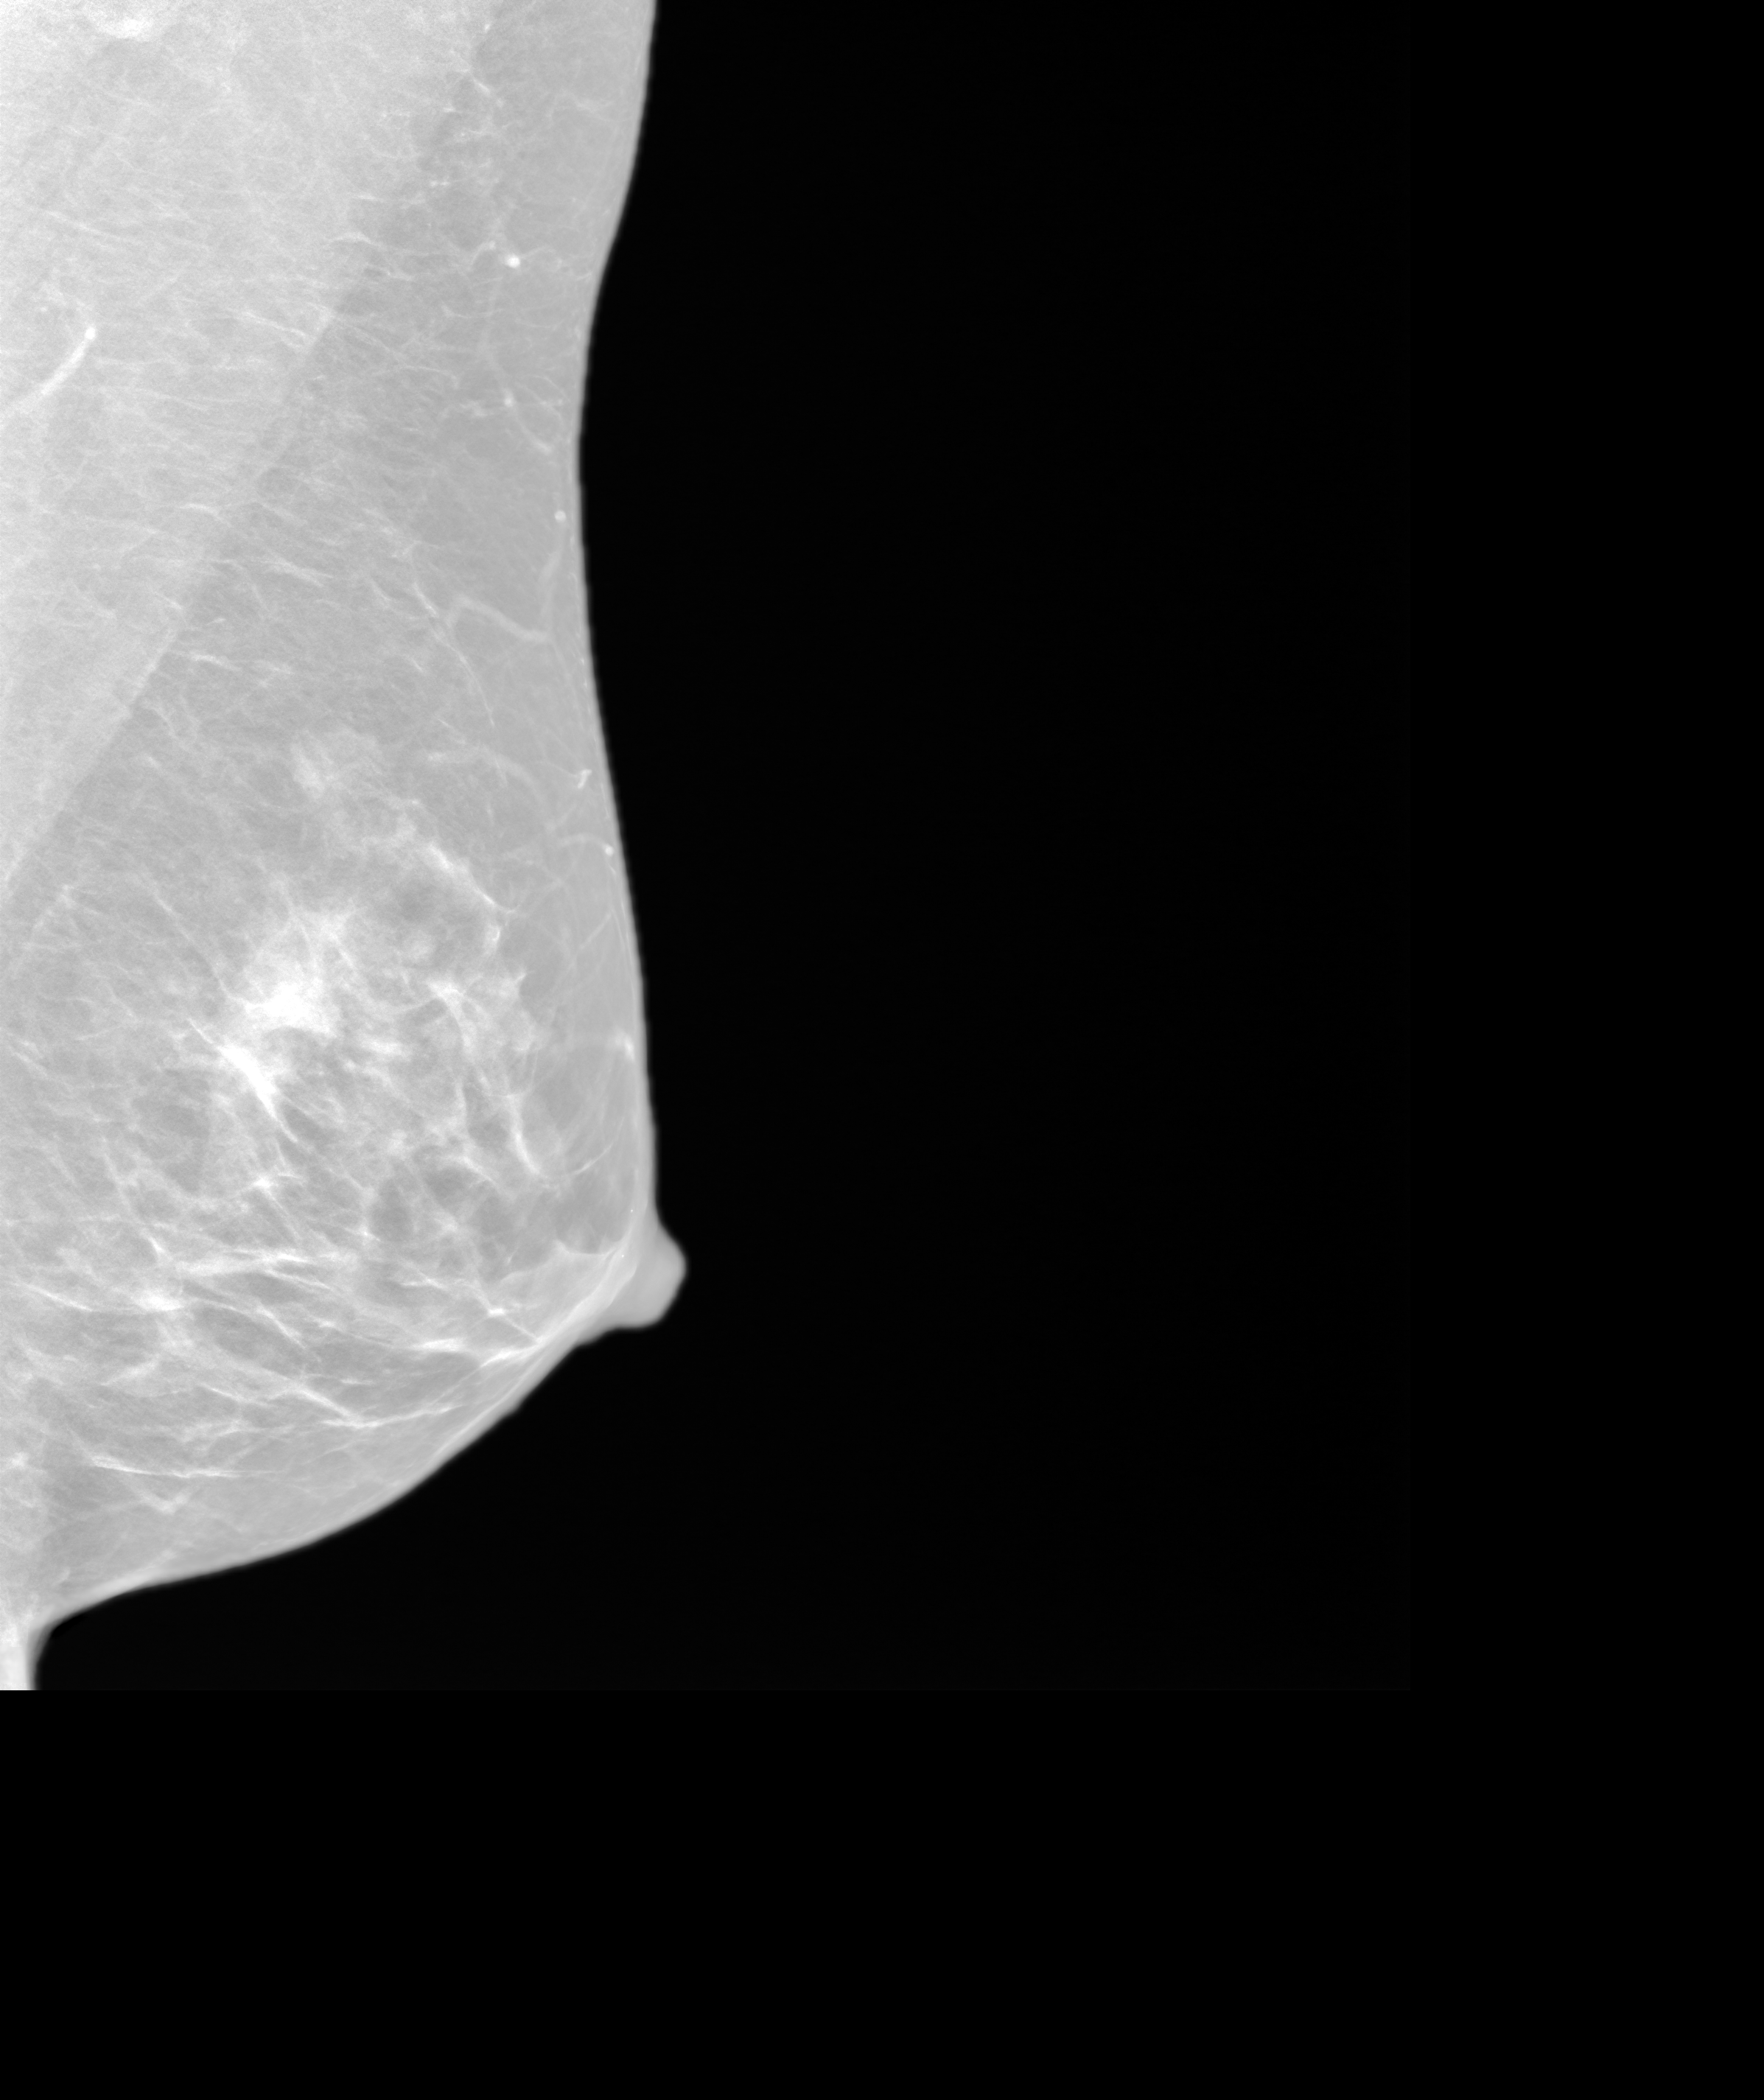
Synthetic 2-D view generated from a tomosynthesis acquisition (not an FFDM exposure); left breast; MLO view; screening examination; system: SenoIris_1SP1.1(421). Patient aged 43 years (female).
BI-RADS breast density category at the screening exam (both breasts, scale 1–4): 2. Final BI-RADS category for the screening round (tomosynthesis exam, both breasts): category 1. Recall: no recall after this screen.